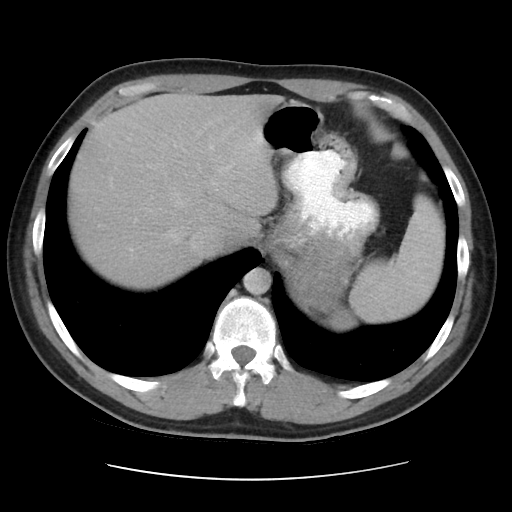
Contrast-enhanced abdominal CT, one axial slice; slice 37 of 48 in the series (ordered by position); reconstruction kernel STANDARD; 120 kVp; intravenous contrast given; soft-tissue window (W 400 / L 40 HU); 5 mm slice thickness; 512 × 512 image matrix. Patient: male, 32 years. From the clinical record (not read from this slice): diagnosis: adrenocortical carcinoma; tumour side: left adrenal; tumour size at pathology: 14 cm; Ki-67 index: 67 %; stage (as recorded): 3.
Annotated regions visible in this slice (semi-automatic segmentation, software-assisted and operator-edited):
- mass: bounding box [x1, y1, x2, y2] px = [291, 243, 348, 312]